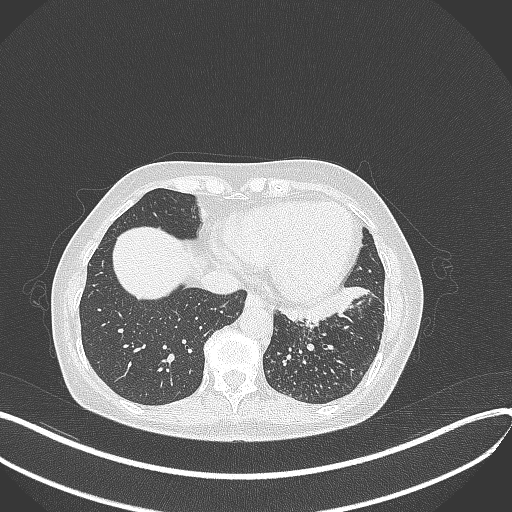
Chest CT, one axial slice. Position 114 of 429 along the scan axis. Reconstruction kernel B70f. Lung window (W 1500 / L -600 HU). 1 mm slice thickness. 512 × 512 image matrix, field of view 400 × 400 mm. Female patient, age 63 years. From the clinical record (not read from this slice): clinical TNM (as recorded): T1b N0 M0; histopathological grade: G2-3.
Annotated regions visible in this slice (bounding box drawn by a radiologist):
- lung tumour (recorded histology: adenocarcinoma): bounding box [x1, y1, x2, y2] px = [282, 284, 369, 330]